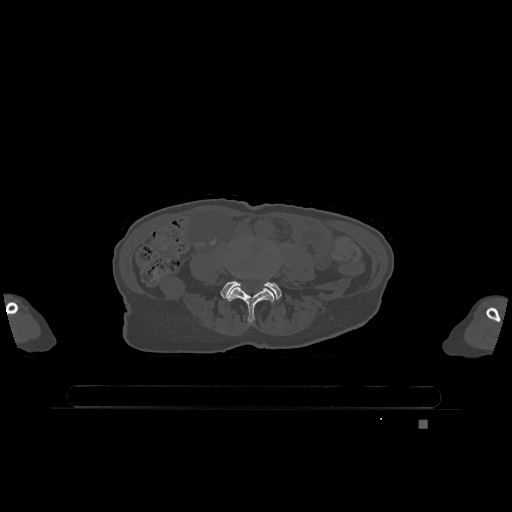
CT including the spine, one axial slice. Bone window (W 1800 / L 400 HU). 0.5 mm slice thickness. 512 × 512 image matrix, field of view 500 × 500 mm. Patient: female, 74 years. Case-level facts recorded for this patient, not image findings: primary cancer: lung; vertebrae with lytic lesions (as recorded): T1, T4, T5, T6, L4, L5.
Annotated regions visible in this slice (semi-automatically segmented with operator editing):
- L4 vertebra: box from (x=228, y=283) to (x=276, y=323) px
- L5 vertebra: (x=220, y=281)–(x=282, y=301)